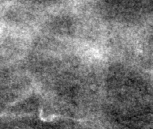
Cropped region of a digitized screen-film mammogram centred on a radiologist-marked abnormality, right breast, CC view.
Marked abnormality: calcifications, morphology fine linear branching; BI-RADS assessment category 2; benign; no additional work-up was recommended (benign without callback).